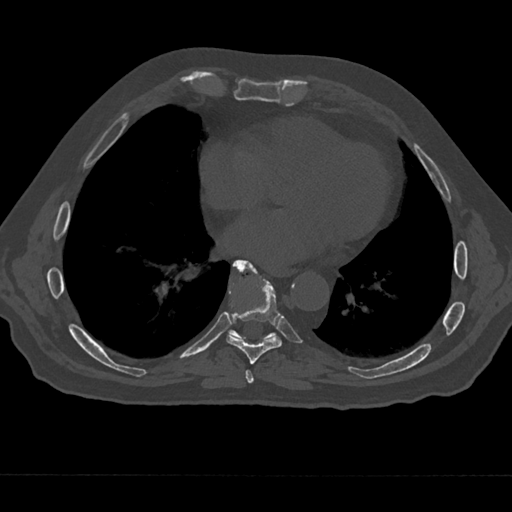
CT including the spine, one axial slice; slice 302 of 797 in the series (ordered by position); reconstruction kernel Br40s/3; 120 kVp; bone window (W 1800 / L 400 HU); 0.5 mm slice thickness; 512 × 512 image matrix, field of view 377 × 377 mm. Patient: male, 75 years. Case-level facts recorded for this patient, not image findings: primary cancer: renal.
Outlined on this slice (semi-automatic segmentation, software-assisted and operator-edited):
- T7 vertebra: bounding box [x1, y1, x2, y2] px = [241, 368, 255, 384]
- T8 vertebra: [226, 263, 282, 364]
- T9 vertebra: [229, 259, 276, 340]